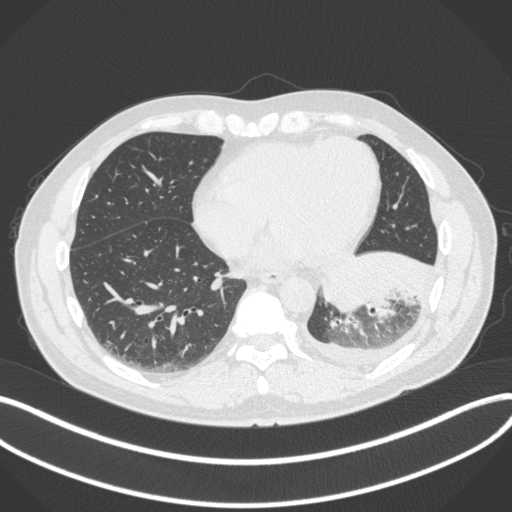
Chest CT, one axial slice. Position 120 of 350 along the scan axis. Reconstruction kernel B31f. 120 kVp. Lung window (W 1500 / L -600 HU). 512 × 512 image matrix, field of view 400 × 400 mm. Male patient, age 58 years. From the clinical record (not read from this slice): clinical TNM (as recorded): T3 N1 M1b; histopathological grade: G3.
Annotated regions visible in this slice (rectangle marked by the reading radiologist):
- lung tumour (recorded histology: small cell carcinoma): bounding box (x1, y1, x2, y2) in pixels: (316, 251, 435, 316)